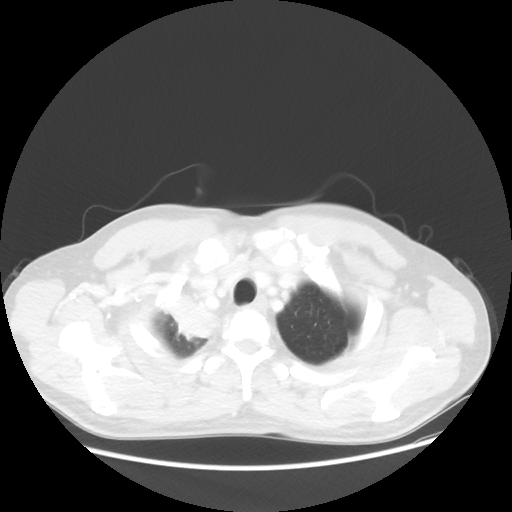
Chest CT, one axial slice. Slice 49 of 56 in the series (ordered by position). Reconstruction kernel STANDARD. 100 kVp. Lung window (W 1500 / L -600 HU). 5 mm slice thickness. 512 × 512 image matrix. Patient: male, 60 years. Case-level facts recorded for this patient, not image findings: clinical TNM (as recorded): T2a N1 M0.
Outlined on this slice (bounding box drawn by a radiologist):
- lung tumour (recorded histology: squamous cell carcinoma): bounding box [x1, y1, x2, y2] px = [157, 286, 221, 345]